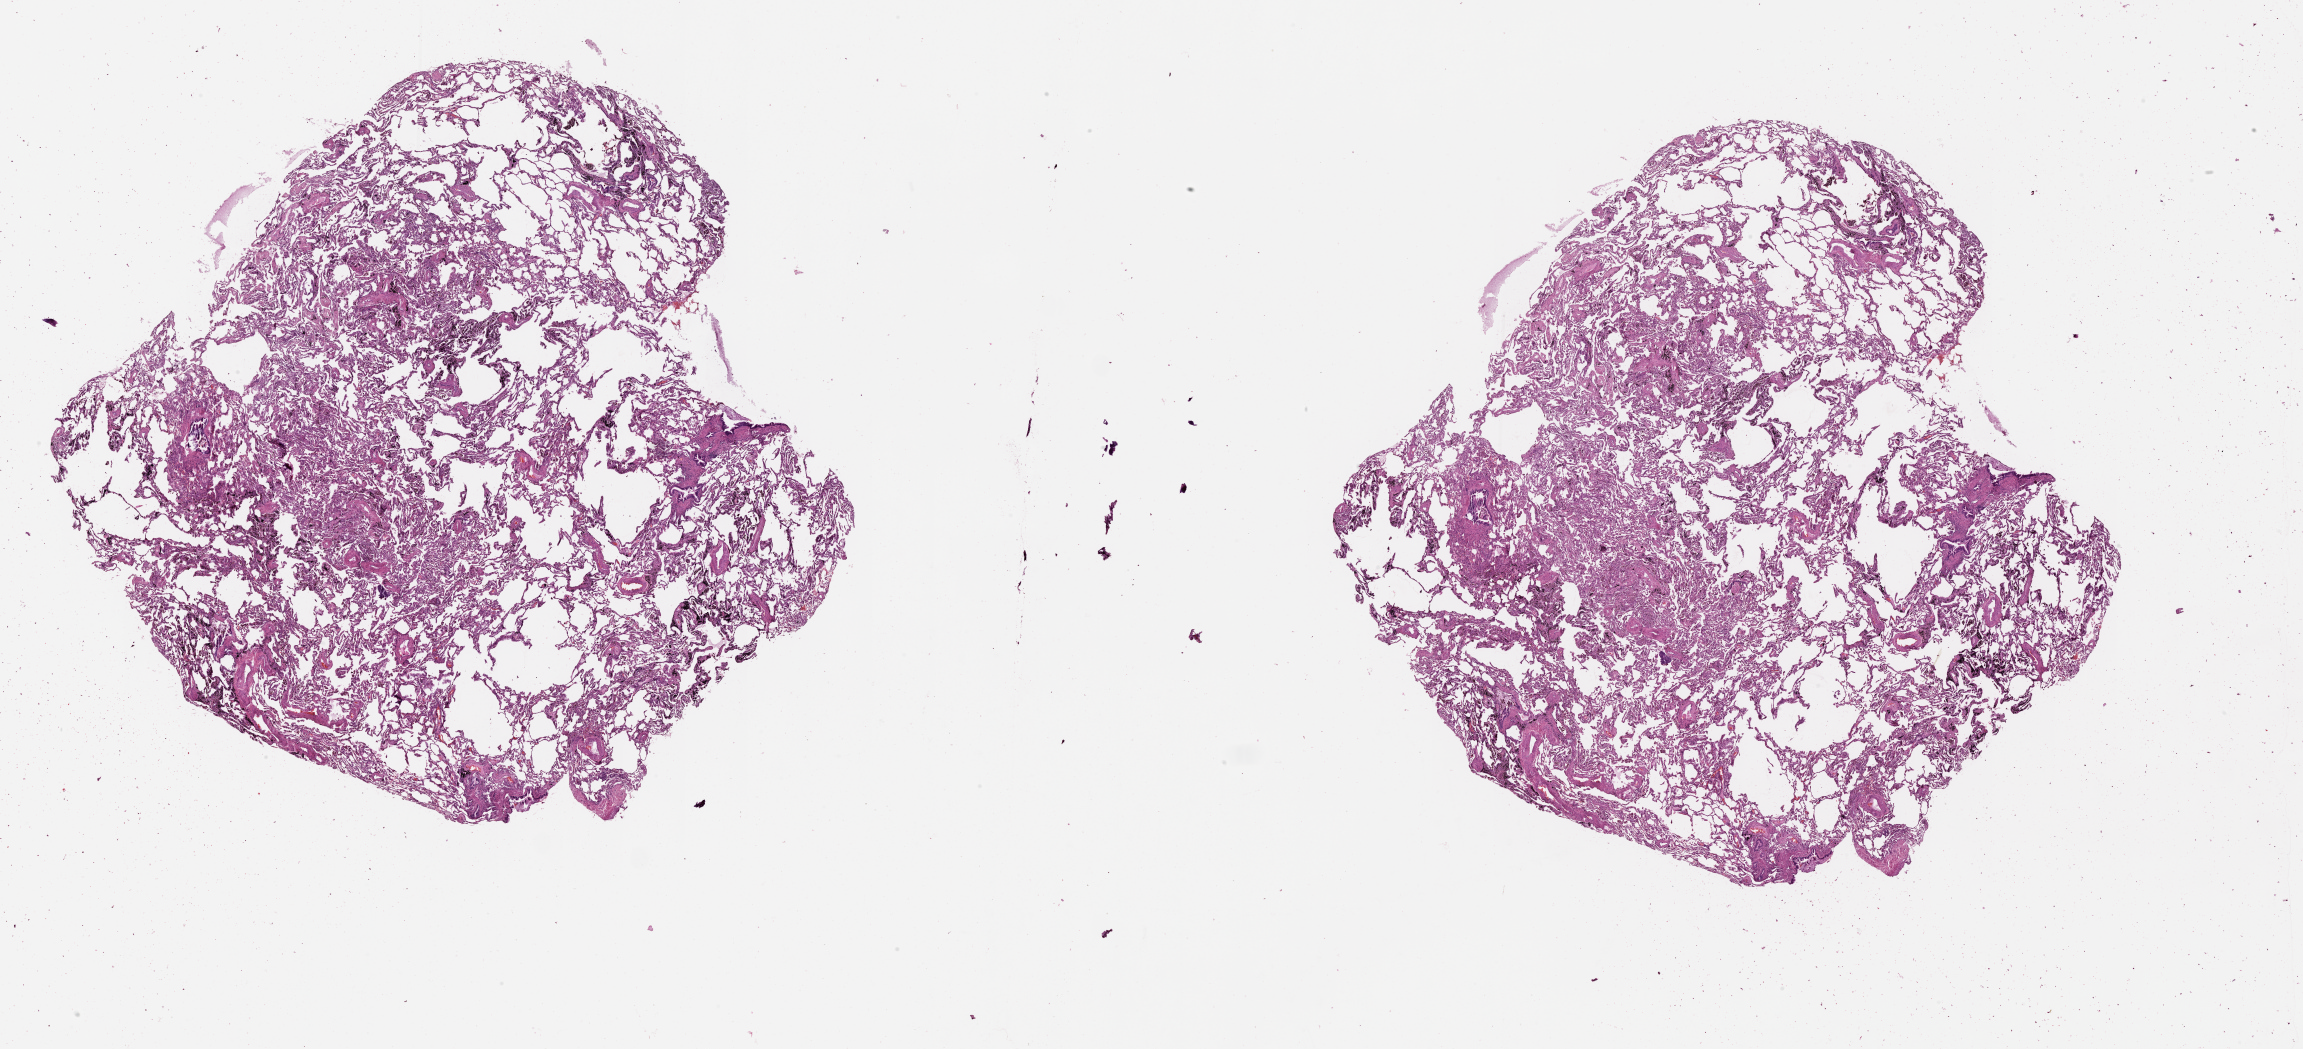
Hematoxylin and eosin (H&E) stained whole-slide image — whole scanned area (about 37.1 x 16.9 mm, from a 20x scan) shown as a low-resolution overview, normal (non-tumour) tissue sample, lung. Male, 59 y/o.
This section: normal (non-tumour) tissue from the same patient. Patient diagnosis (cohort enrolment): squamous cell carcinoma (lung).